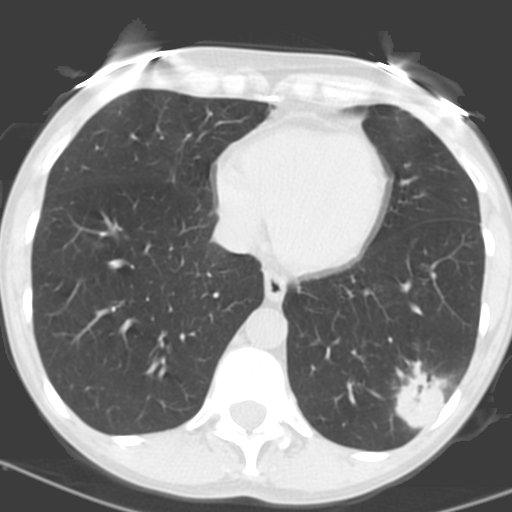
Low-dose screening chest CT, one axial slice. 120 kVp. Lung window (W 1500 / L -600 HU). 3.2 mm slice thickness. 512 × 512 image matrix, field of view 262 × 262 mm.
Outlined on this slice (manually delineated by an expert):
- lesion 1 (tumor, lower lobe of left lung): bounding box (x1, y1, x2, y2) in pixels: (393, 360, 444, 430)